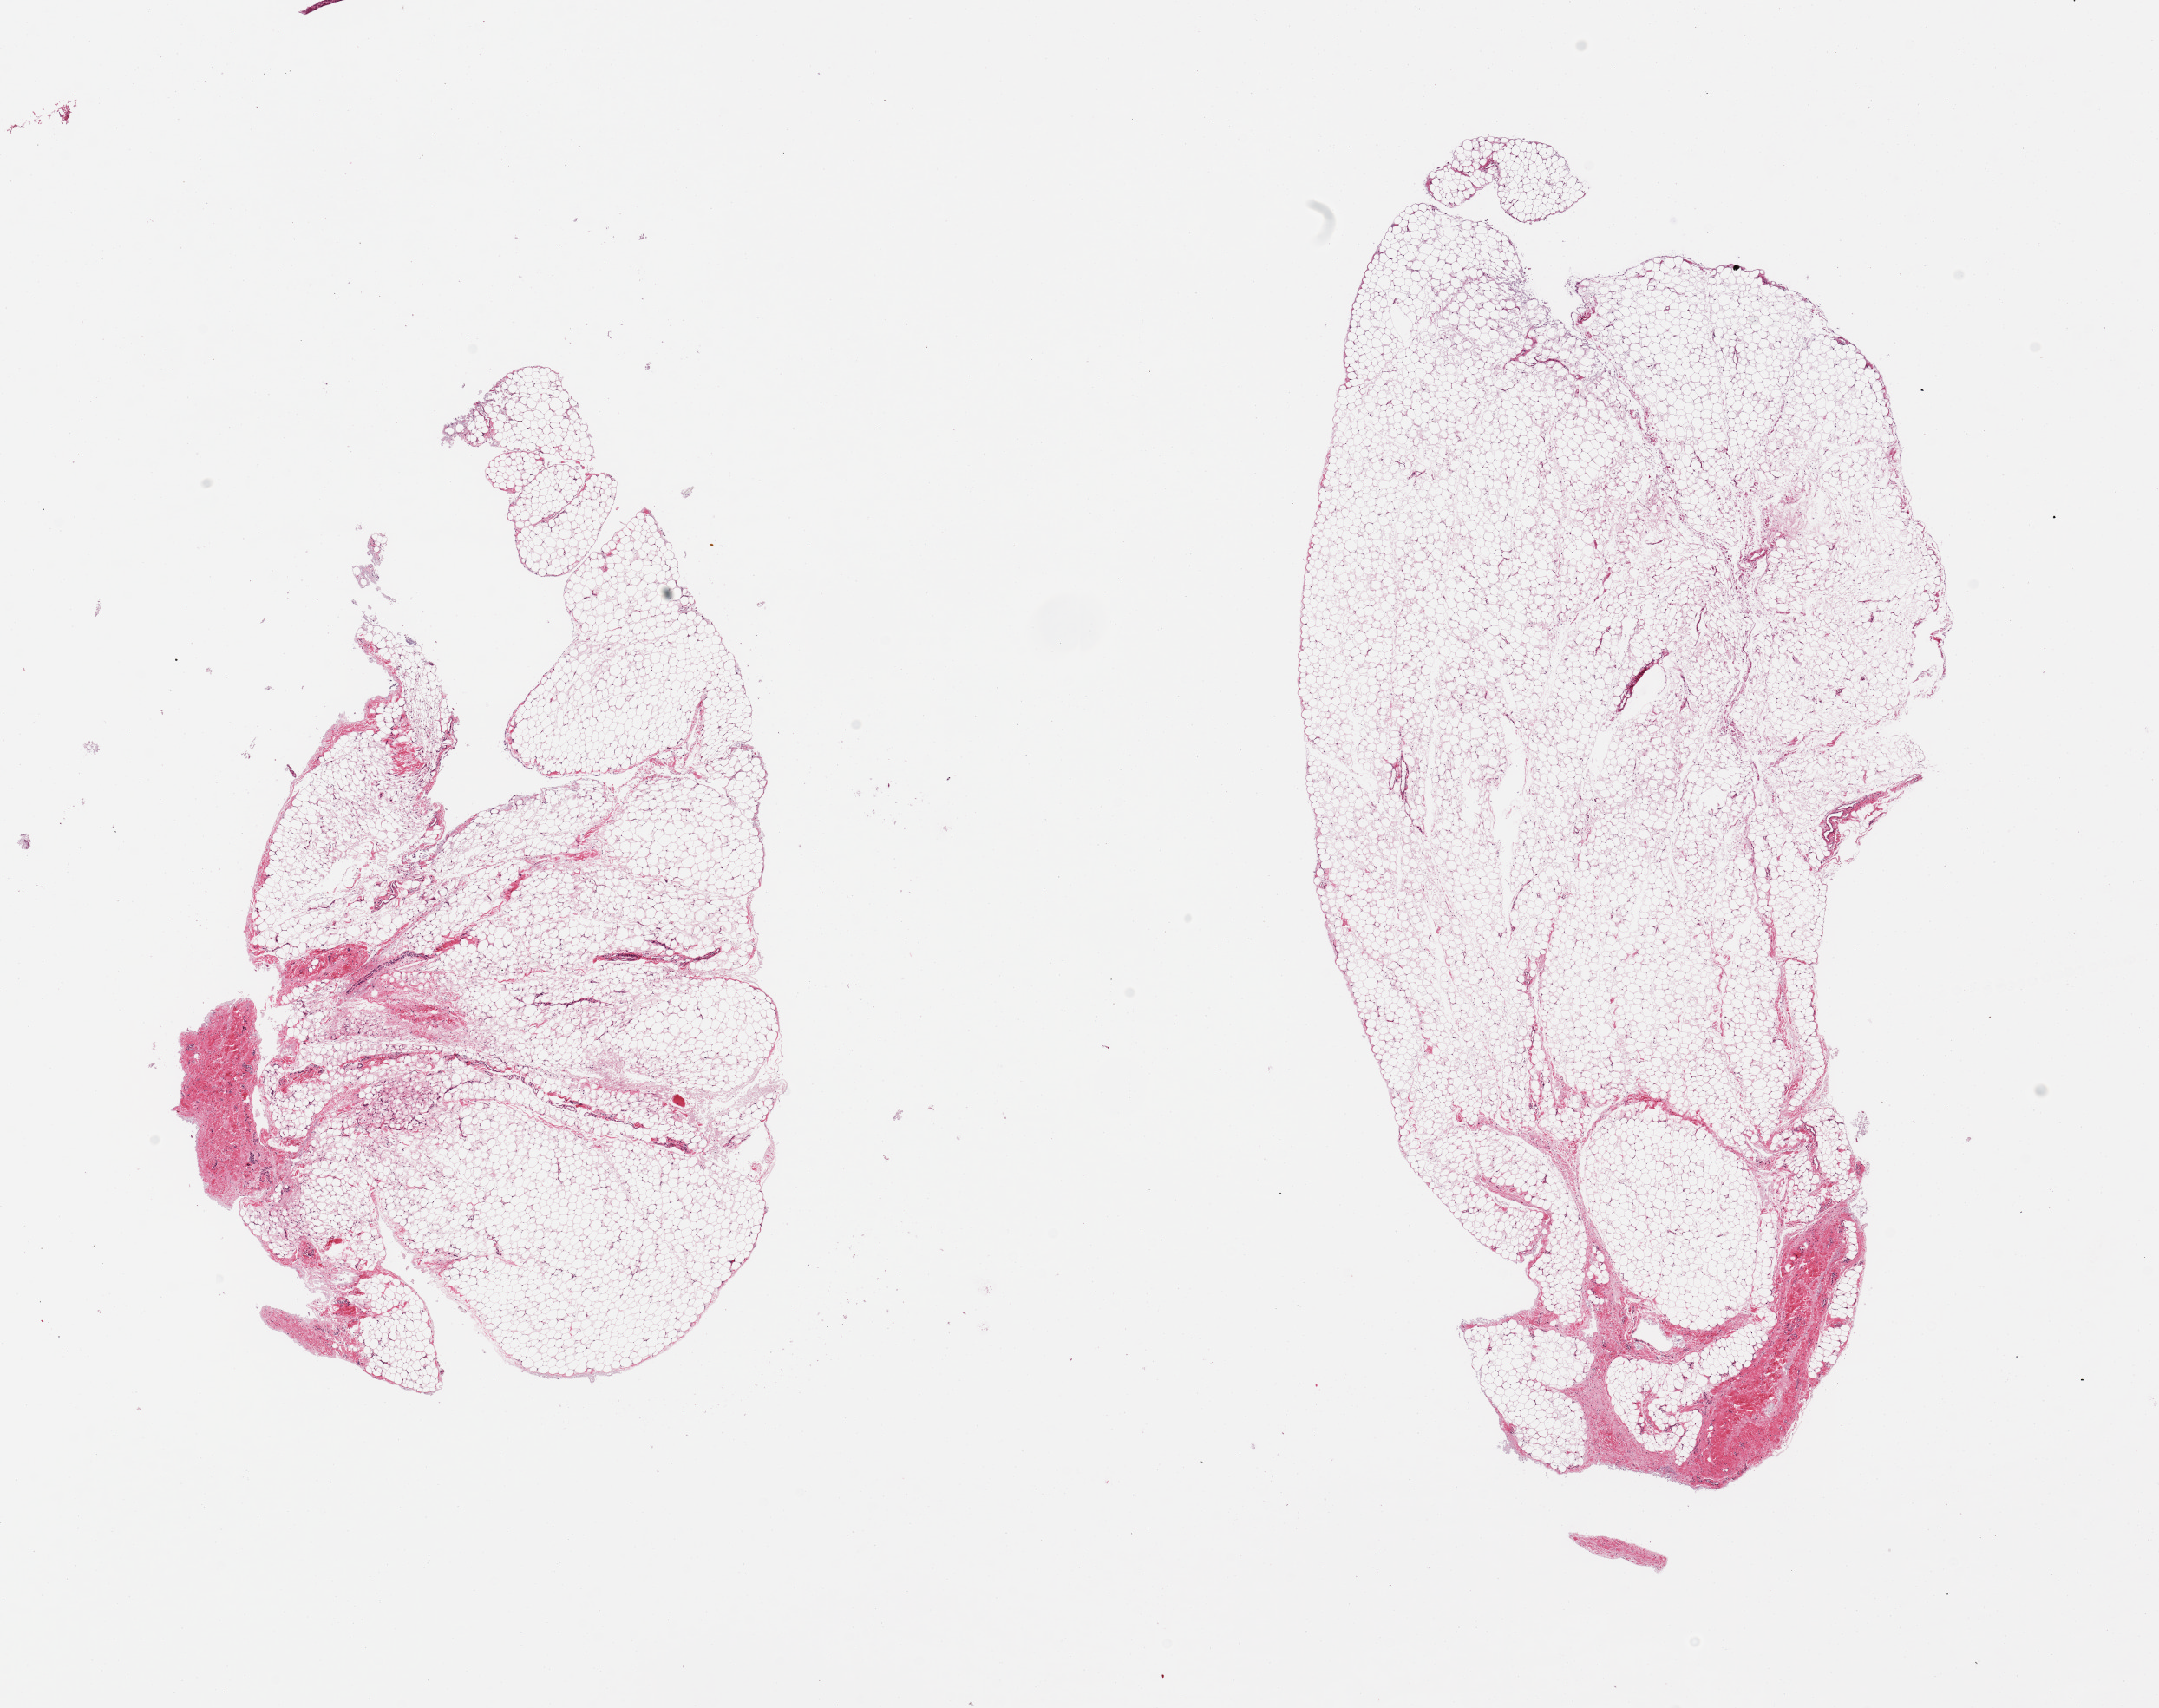
Hematoxylin and eosin (H&E) whole-slide image, whole scanned area (about 19.7 x 15.6 mm, from a 20x scan) shown as a low-resolution overview. PAXgene-fixed, paraffin-embedded tissue. Section of omentum (target tissue). Tissue donor sample.
- review note (as recorded): 2 pieces; ~10% fibrovascular component